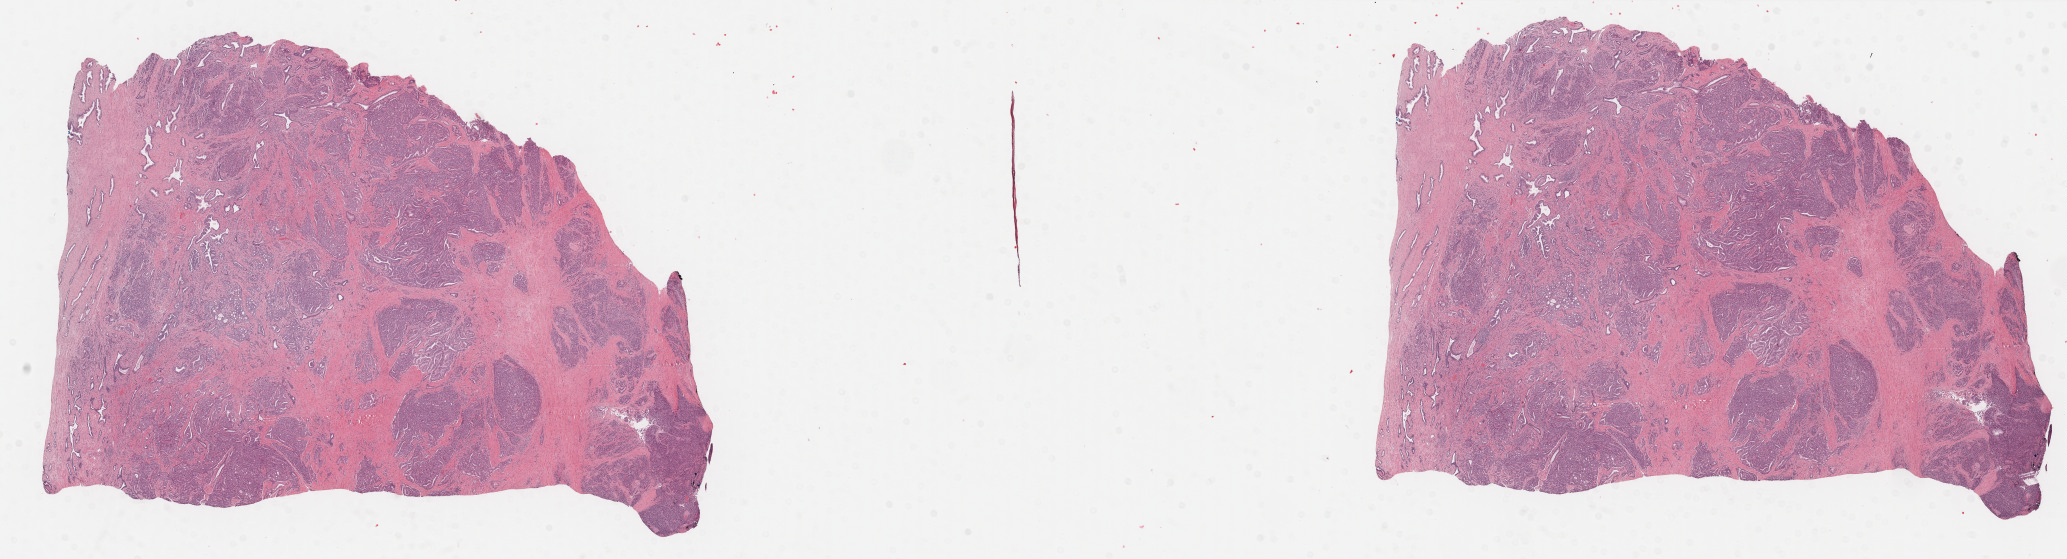
Whole-slide histology image, H&E, shown as a low-resolution overview of the whole scanned area (about 32.7 x 8.8 mm), FFPE section, prostate, primary tumour sample. Male, age 65 years at initial diagnosis.
Pathologic diagnosis: Adenocarcinoma, NOS (prostate gland).